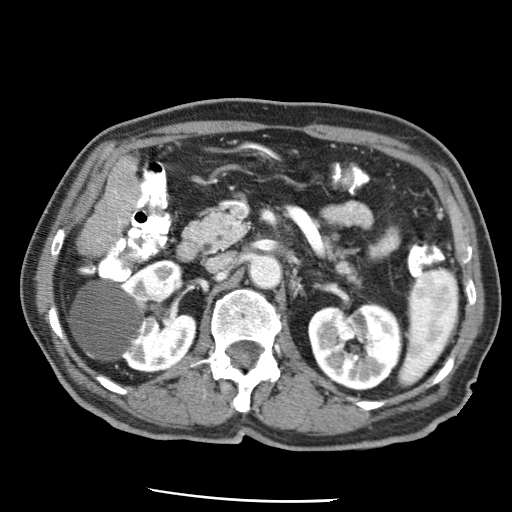
Contrast-enhanced abdominal CT (liver protocol), one axial slice; 120 kVp; soft-tissue window (W 400 / L 40 HU); 2.5 mm slice thickness; 512 × 512 image matrix. Case-level facts recorded for this patient, not image findings: diagnosis: hepatocellular carcinoma (patient treated with transarterial chemoembolisation; whether this scan precedes or follows treatment is not stated here); TNM stage (as recorded): Stage-IIIA.
Annotated regions visible in this slice (semi-automatically segmented with operator editing):
- liver parenchyma outside the tumour (the mass and vessels are separate outlines, so this box may not span the whole liver): box from (x=86, y=158) to (x=138, y=249) px
- liver vessels: (x=113, y=166)–(x=135, y=225)